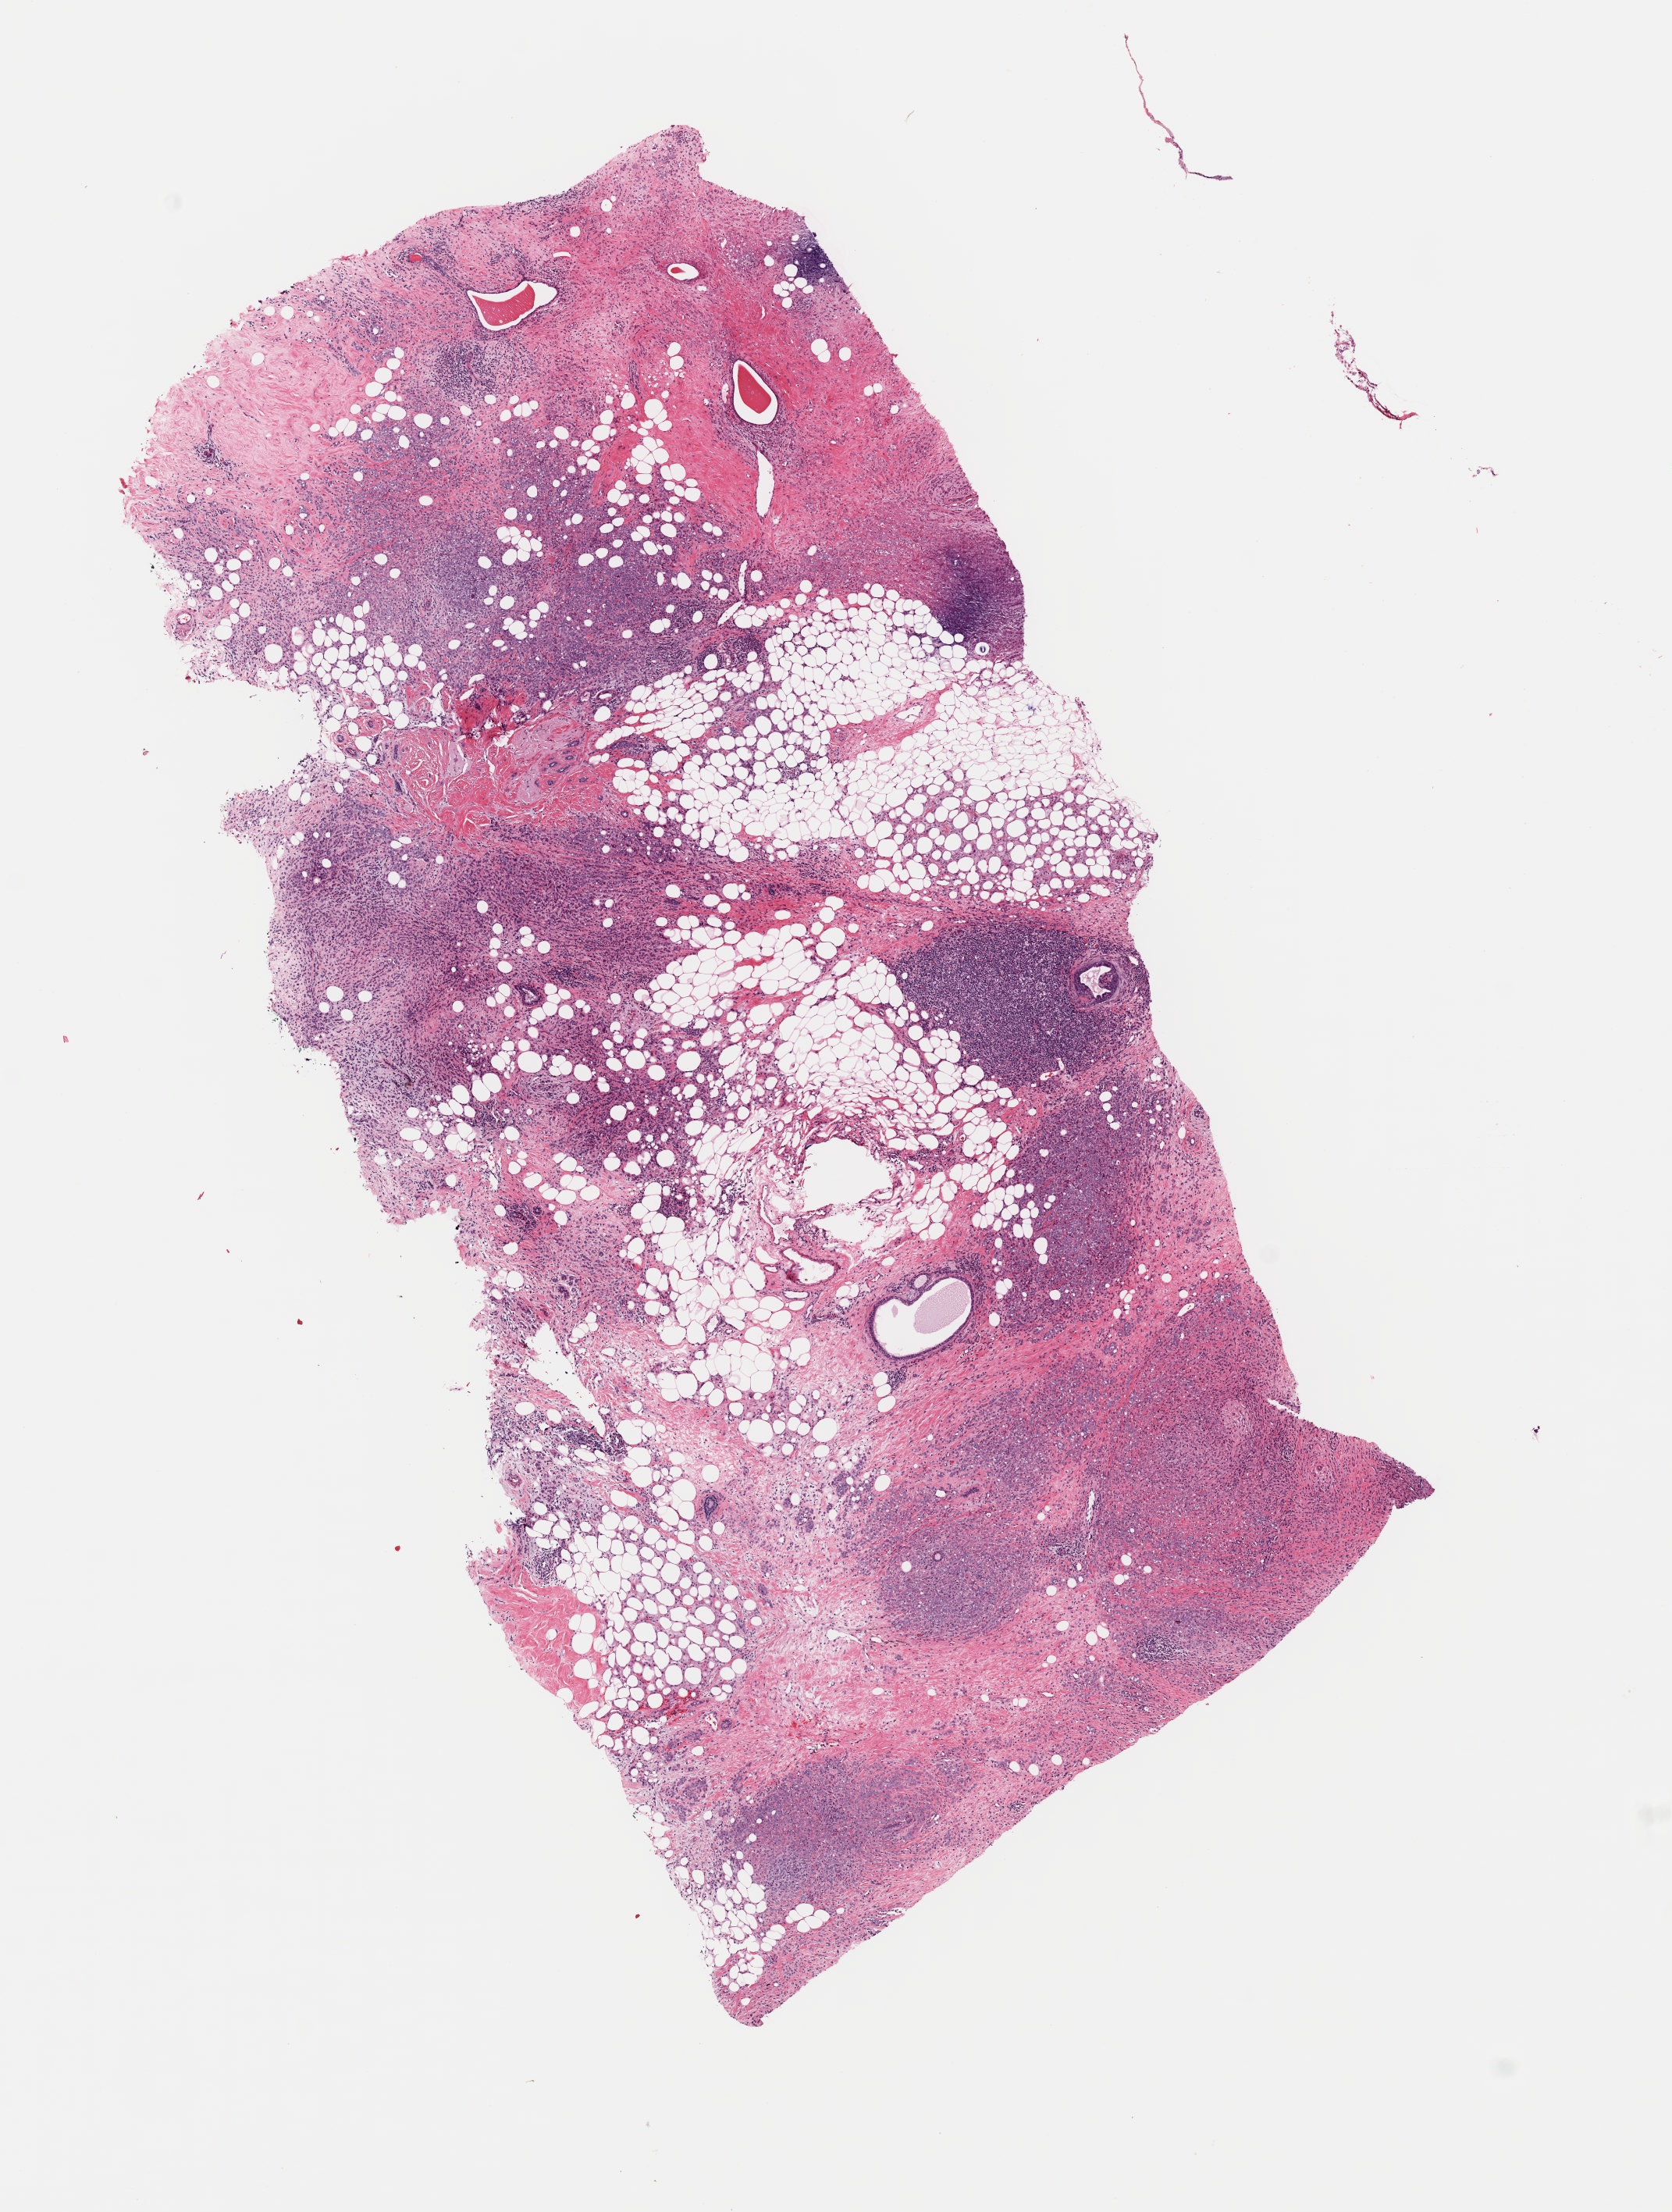
Whole-slide histology image, Hematoxylin and eosin (H&E) stained — shown as a low-resolution overview of the whole scanned area (about 8.5 x 11.2 mm). Frozen section. Sample: primary tumour, breast. Female, age 68 years at initial diagnosis. Composition of this section per pathologist review: tumour cells 60%, tumour nuclei 70%, normal cells 5%, stromal cells 35%, necrosis 0%. Inflammatory infiltration, as recorded: lymphocyte infiltration 0%, monocyte infiltration 0%, neutrophil infiltration 0%.
Diagnosis: Lobular carcinoma, NOS. Laterality: left. TNM: T2 N1mi MX. AJCC pathologic stage: IIB (7th edition).